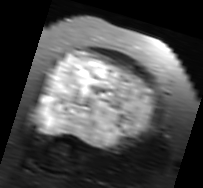
MRI of an extremity soft-tissue mass, one axial slice; slice 47 of 91 in the series (ordered by position); T2-weighted fat-saturated; MR volume resampled by the dataset authors to the PET/CT grid (not the native acquisition matrix); 203 × 188 image matrix, field of view 198 × 184 mm. Female patient. From the clinical record (not read from this slice): histological type: malignant solitary fibrous tumor; grade: intermediate; site of the primary tumour: right thigh.
Outlined on this slice (expert contour drawn on MRI and transferred to this co-registered scan by the dataset authors):
- gross tumour volume including surrounding oedema: bounding box <30,51,159,150> (left, top, right, bottom; pixels)
- gross tumour volume (mass): <35,51,155,146>